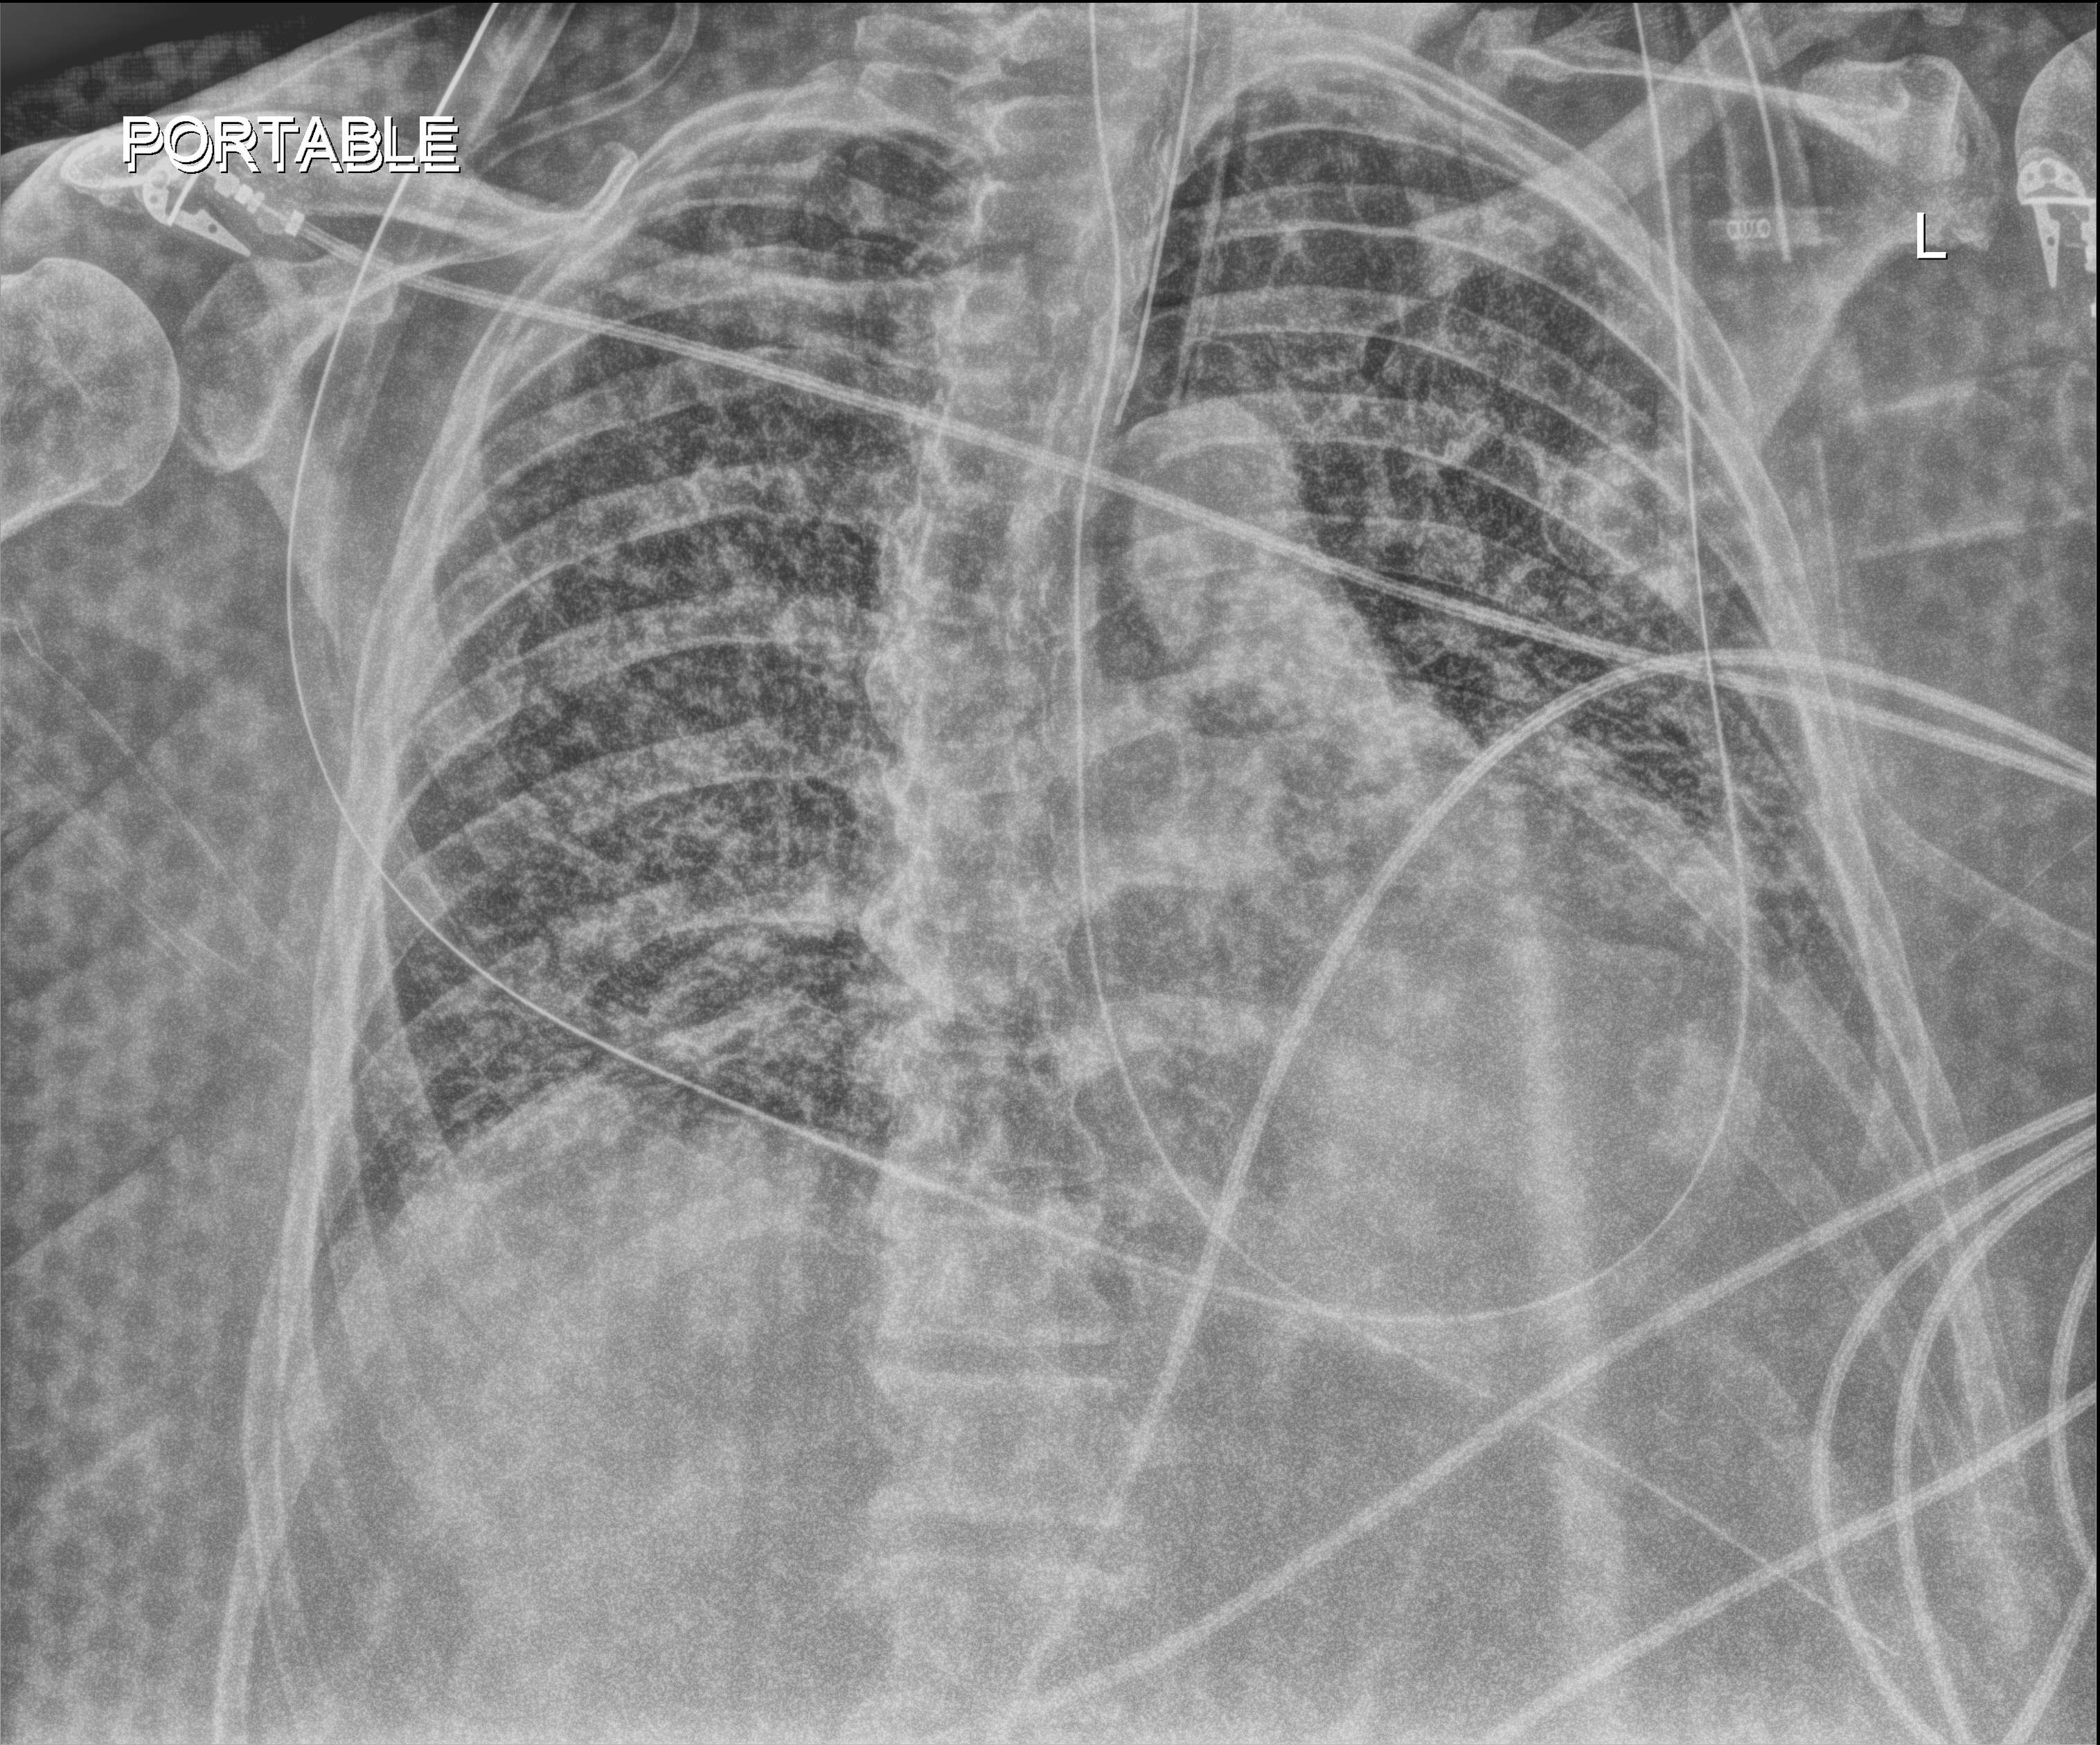
Portable chest radiograph, anteroposterior (AP) projection. Adult patient hospitalised with COVID-19, age 18–59 years.
From the hospital-stay record, not from the radiograph (when in the stay this image was taken is not recorded): admitted to intensive care during this hospital stay: yes; length of hospital stay: 28 days.